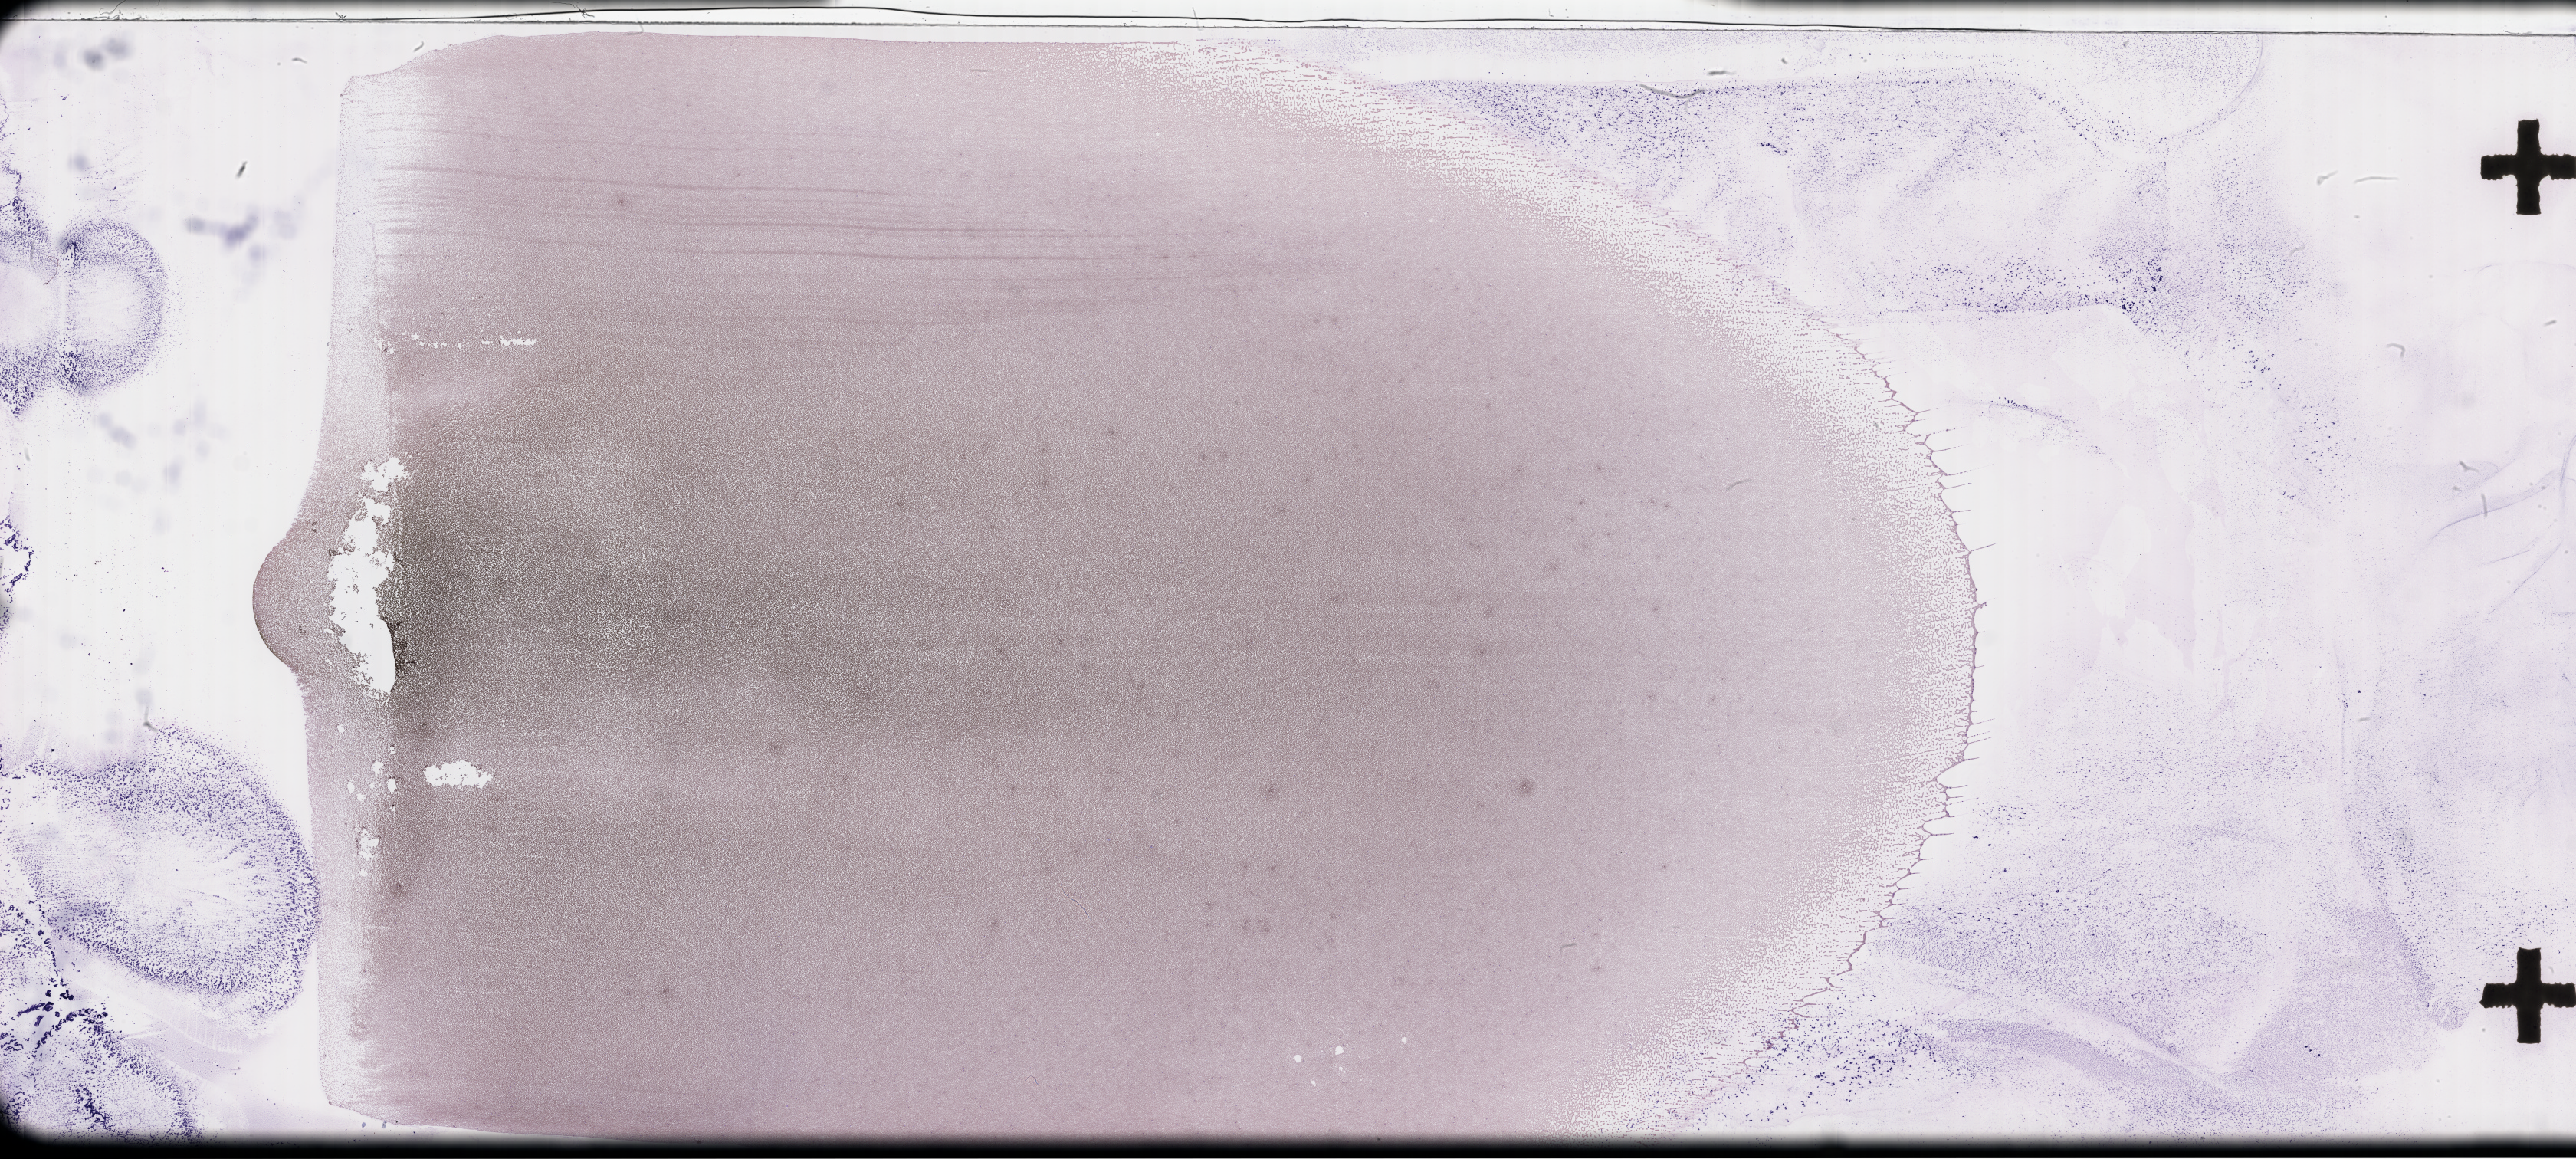
Whole-slide image of a whole blood smear, Wright–Giemsa stain, shown as a low-resolution overview of the whole scanned area (about 54.3 x 24.4 mm), specimen time point: collected on treatment. Patient sex: male.
Patient diagnosis: Plasma Cell Myeloma.